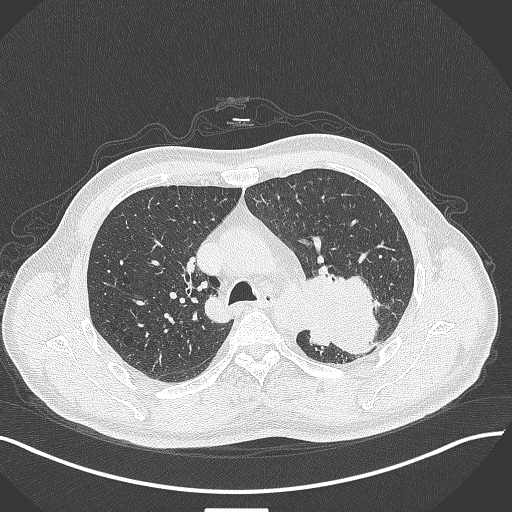
Chest CT, one axial slice; slice 293 of 429 in the series (ordered by position); 120 kVp; lung window (W 1500 / L -600 HU); 512 × 512 image matrix. Patient: male, 55 years. Case-level facts recorded for this patient, not image findings: clinical TNM (as recorded): T3 N0 M1c; histopathological grade: G3.
Outlined on this slice (rectangle marked by the reading radiologist):
- lung tumour (recorded histology: adenocarcinoma): bounding box <294,265,387,353> (left, top, right, bottom; pixels)